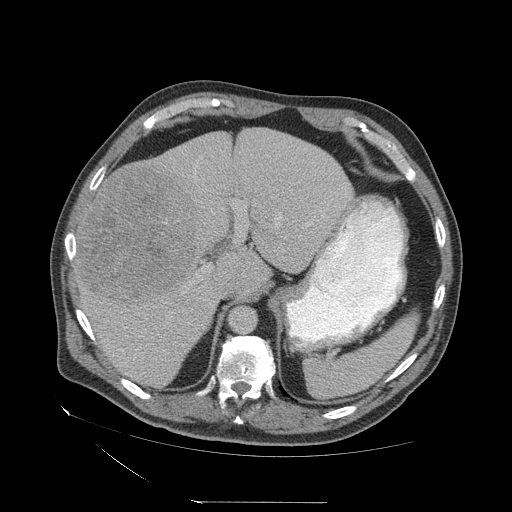
Contrast-enhanced abdominal CT (liver protocol), one axial slice; position 44 of 83 along the scan axis; 140 kVp; soft-tissue window (W 400 / L 40 HU); 512 × 512 image matrix, field of view 460 × 460 mm. From the clinical record (not read from this slice): diagnosis: hepatocellular carcinoma (patient treated with transarterial chemoembolisation; whether this scan precedes or follows treatment is not stated here); TNM stage (as recorded): Stage-I; Child-Pugh class: A; tumour nodularity: uninodular.
Structures marked on this image (semi-automatically segmented with operator editing):
- liver parenchyma outside the tumour (the mass and vessels are separate outlines, so this box may not span the whole liver): box from (x=74, y=128) to (x=352, y=388) px
- mass: (x=80, y=164)–(x=204, y=308)
- liver vessels: (x=88, y=217)–(x=281, y=351)